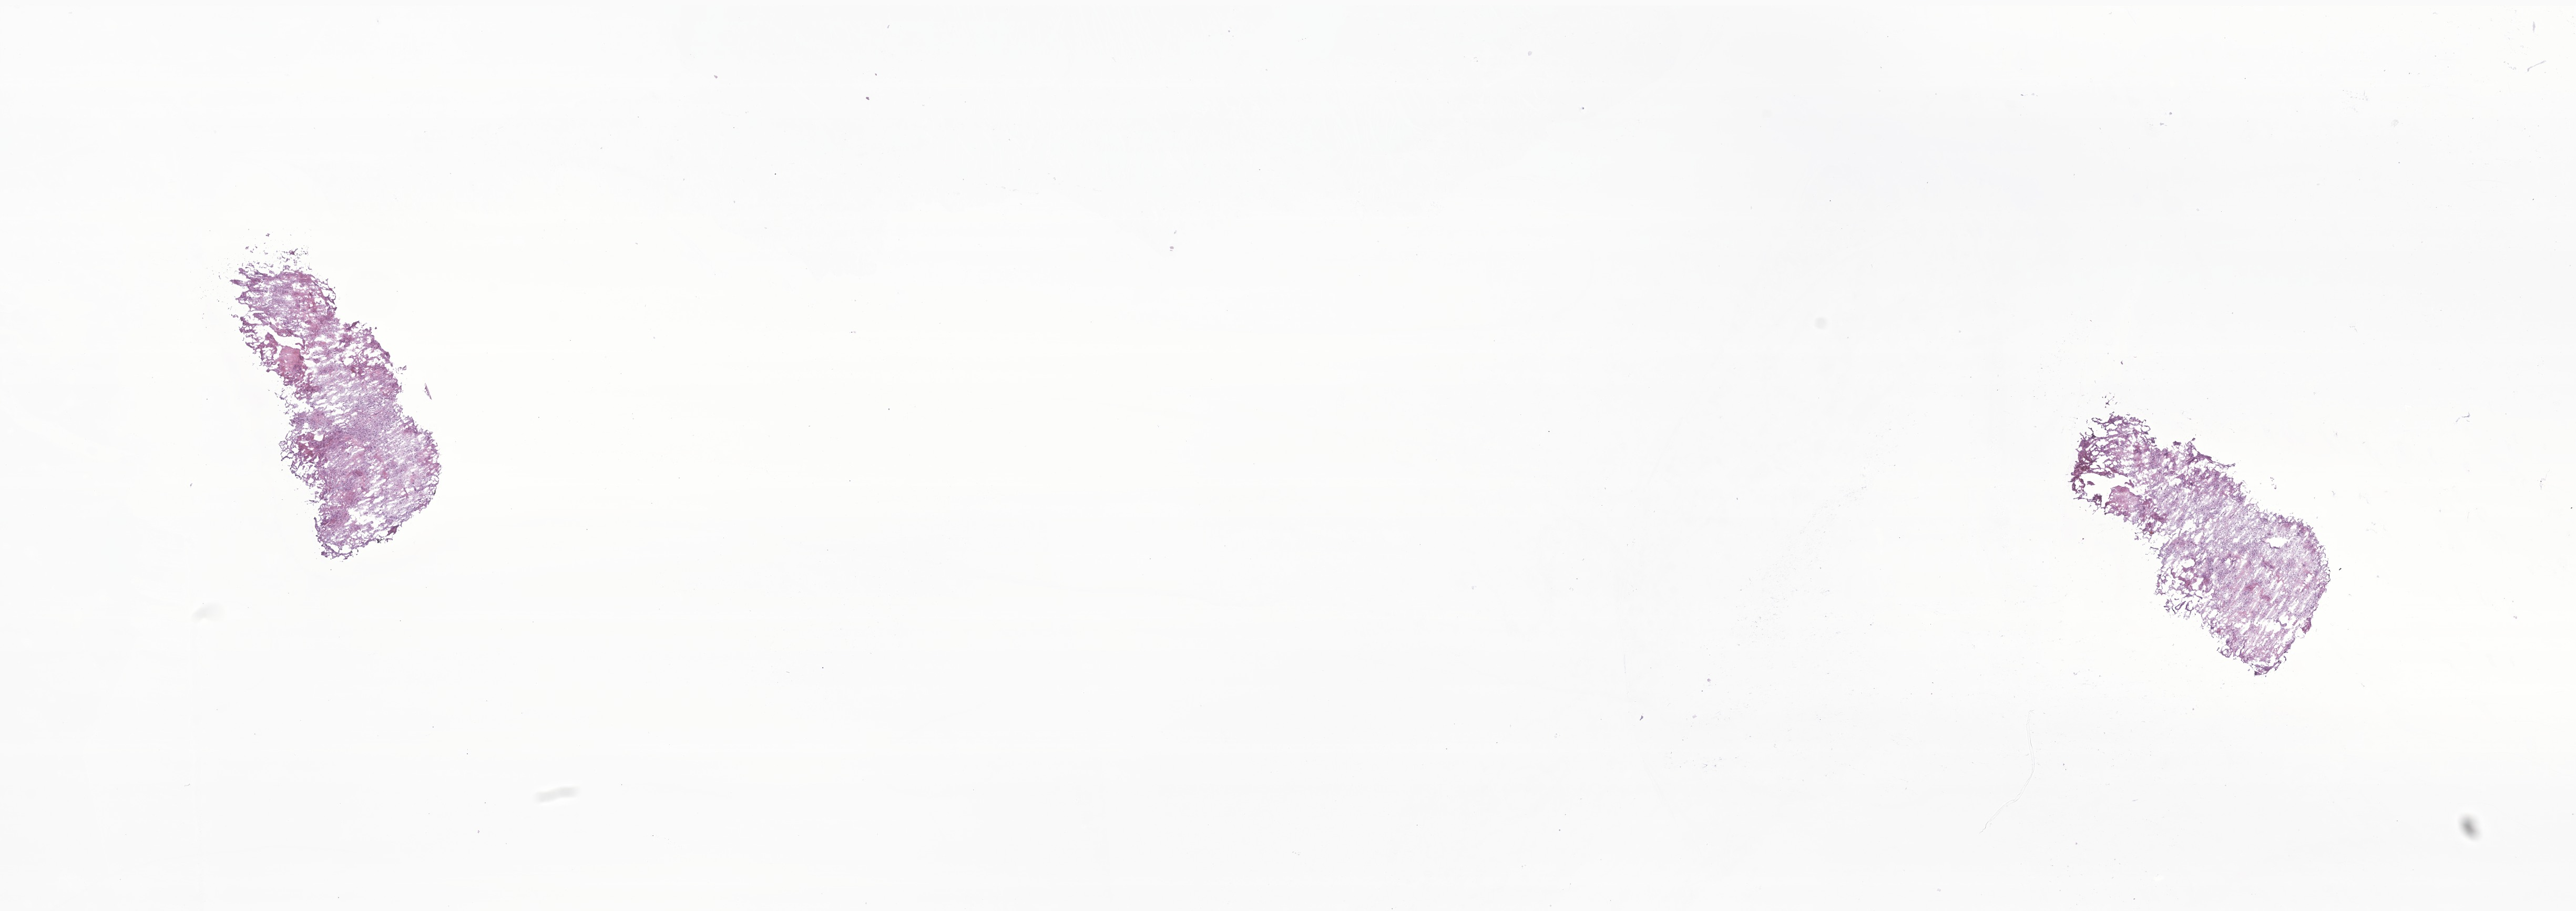
Digitized hematoxylin and eosin (H&E)-stained section of tumor tissue from the brain — low-resolution overview of the scanned area, about 20.7 x 7.3 mm. Frozen section (OCT-embedded). Patient male; age 173 months (14 years 5 months).
- diagnosis (ICD-O-3 morphology term): Glioma, malignant